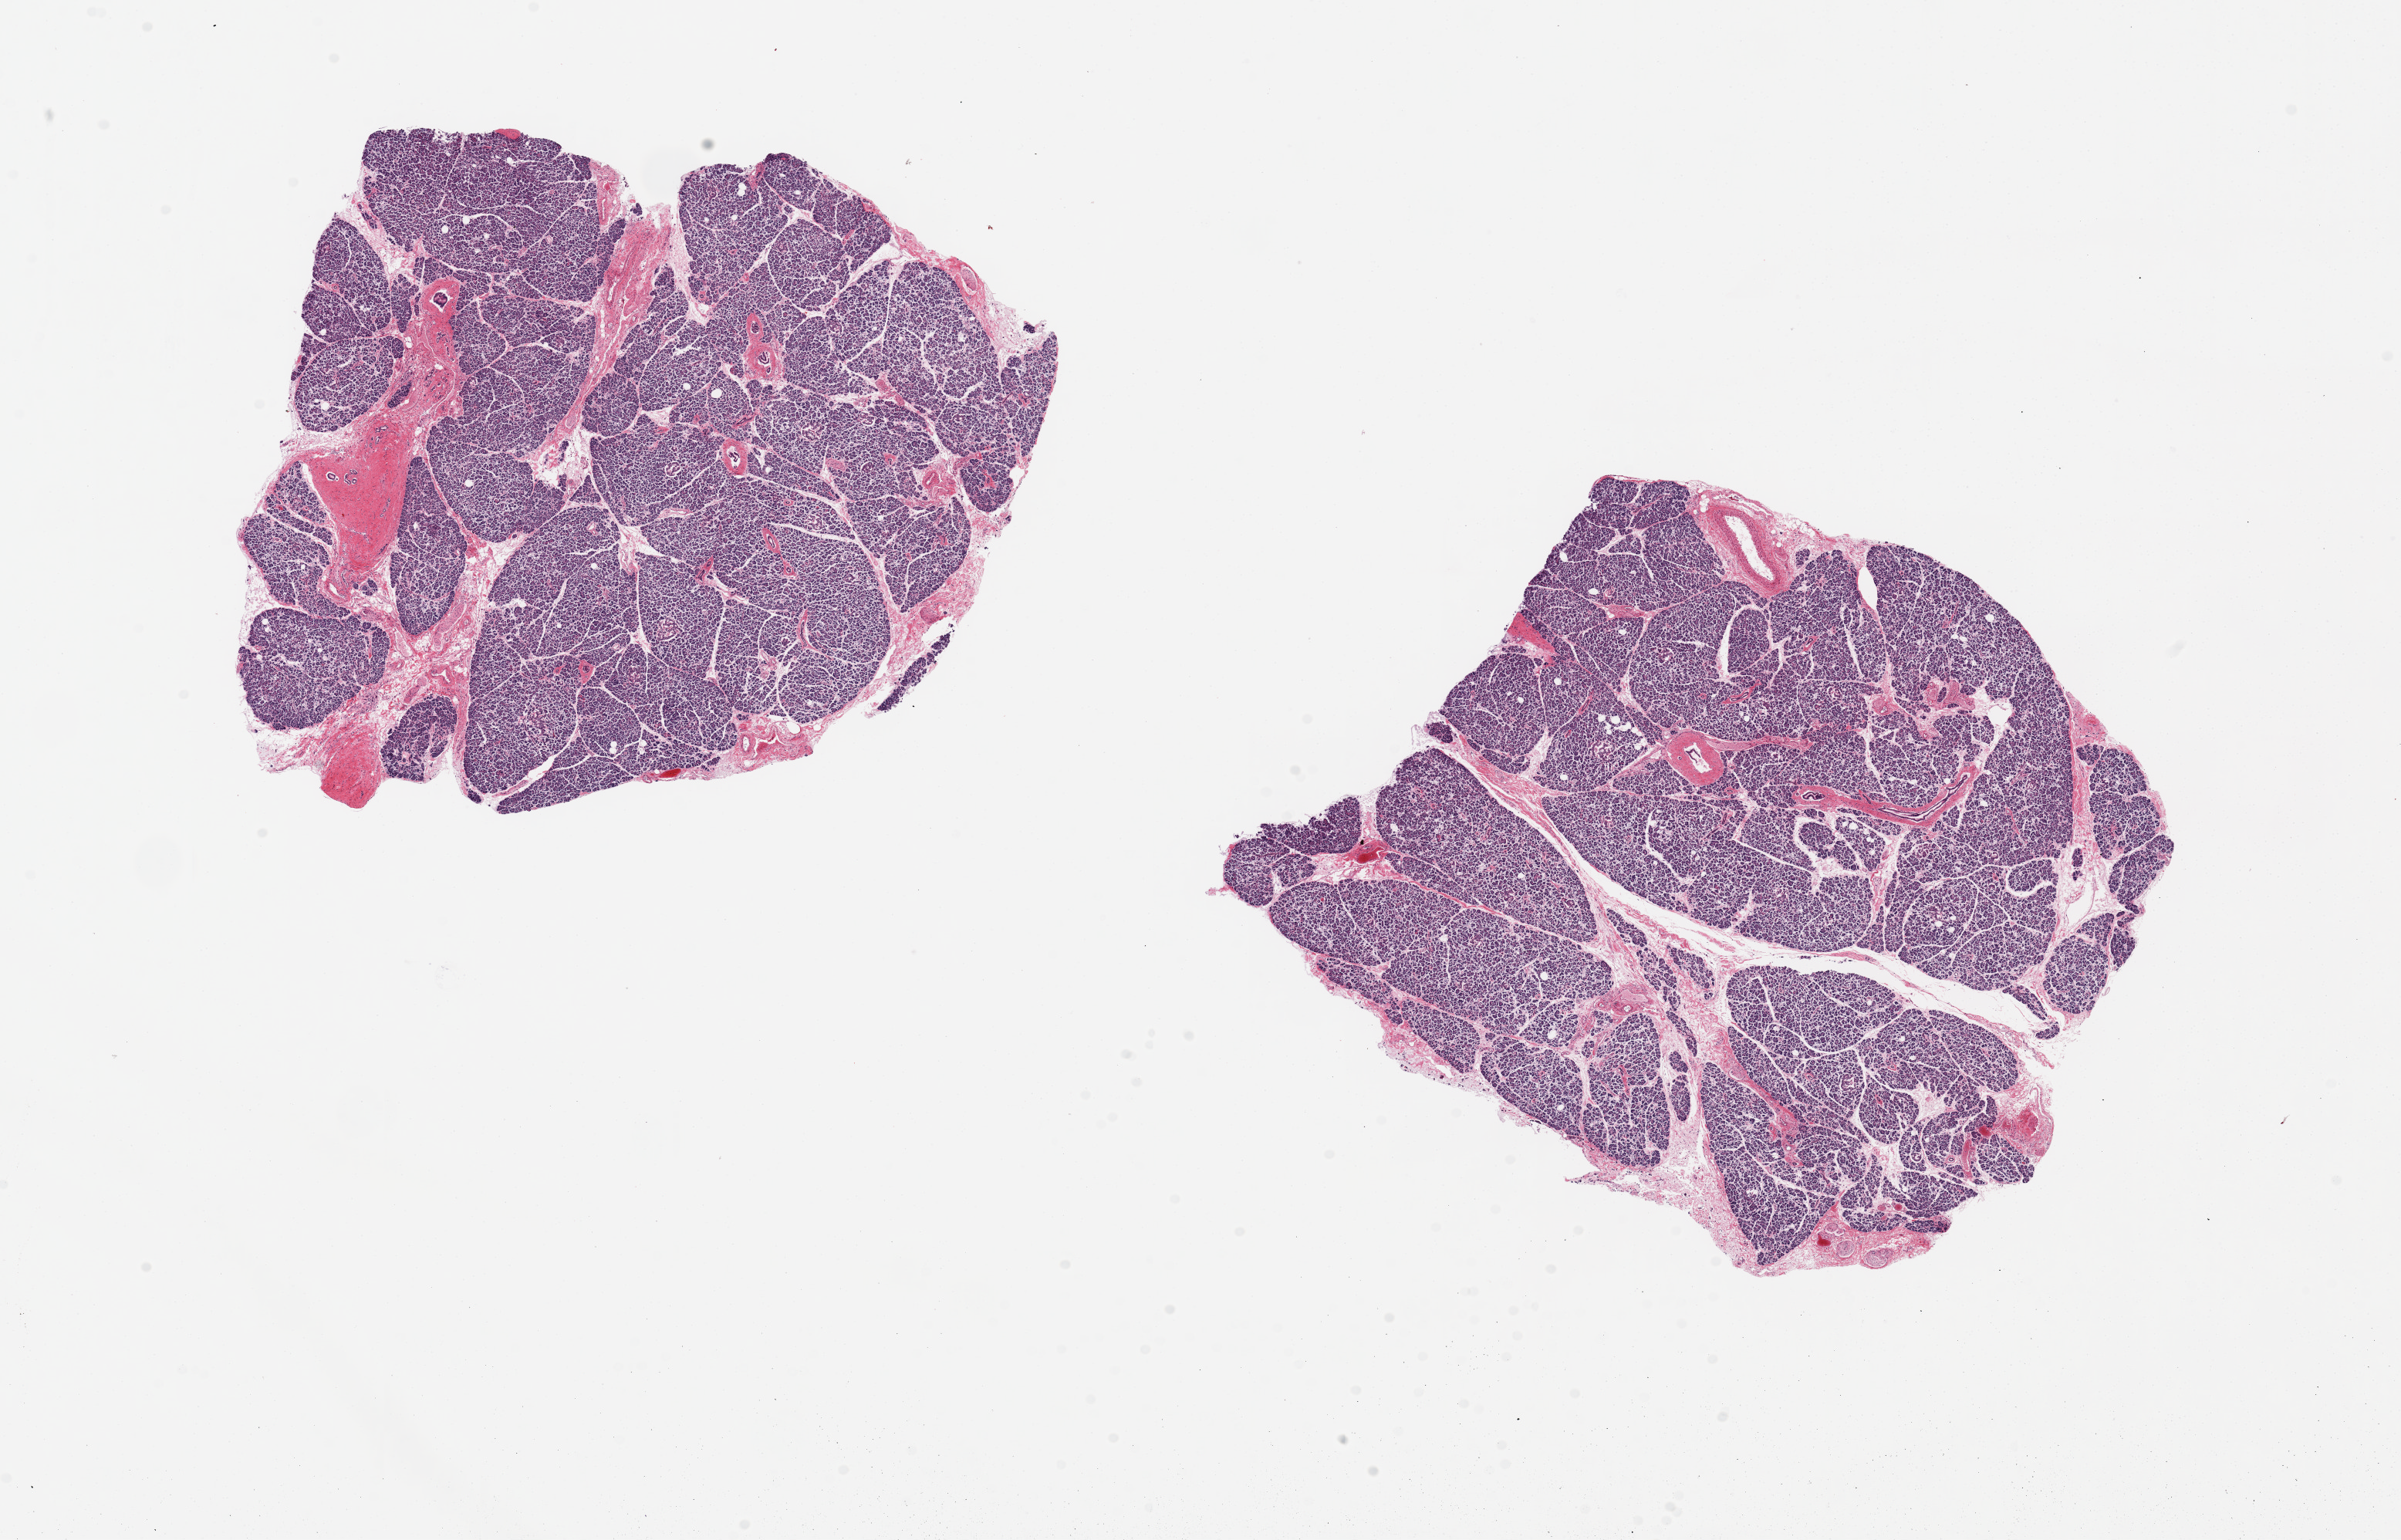
Digitized H&E-stained section, low-resolution overview of the scanned area, about 24.6 x 15.8 mm, PAXgene-fixed, paraffin-embedded tissue, target tissue: pancreas, donor tissue sample. Female donor.
Reviewer comment on this tissue sample: 2 pieces ~7x7mm. Moderate autolysis/aponification, Islets not well visualized.